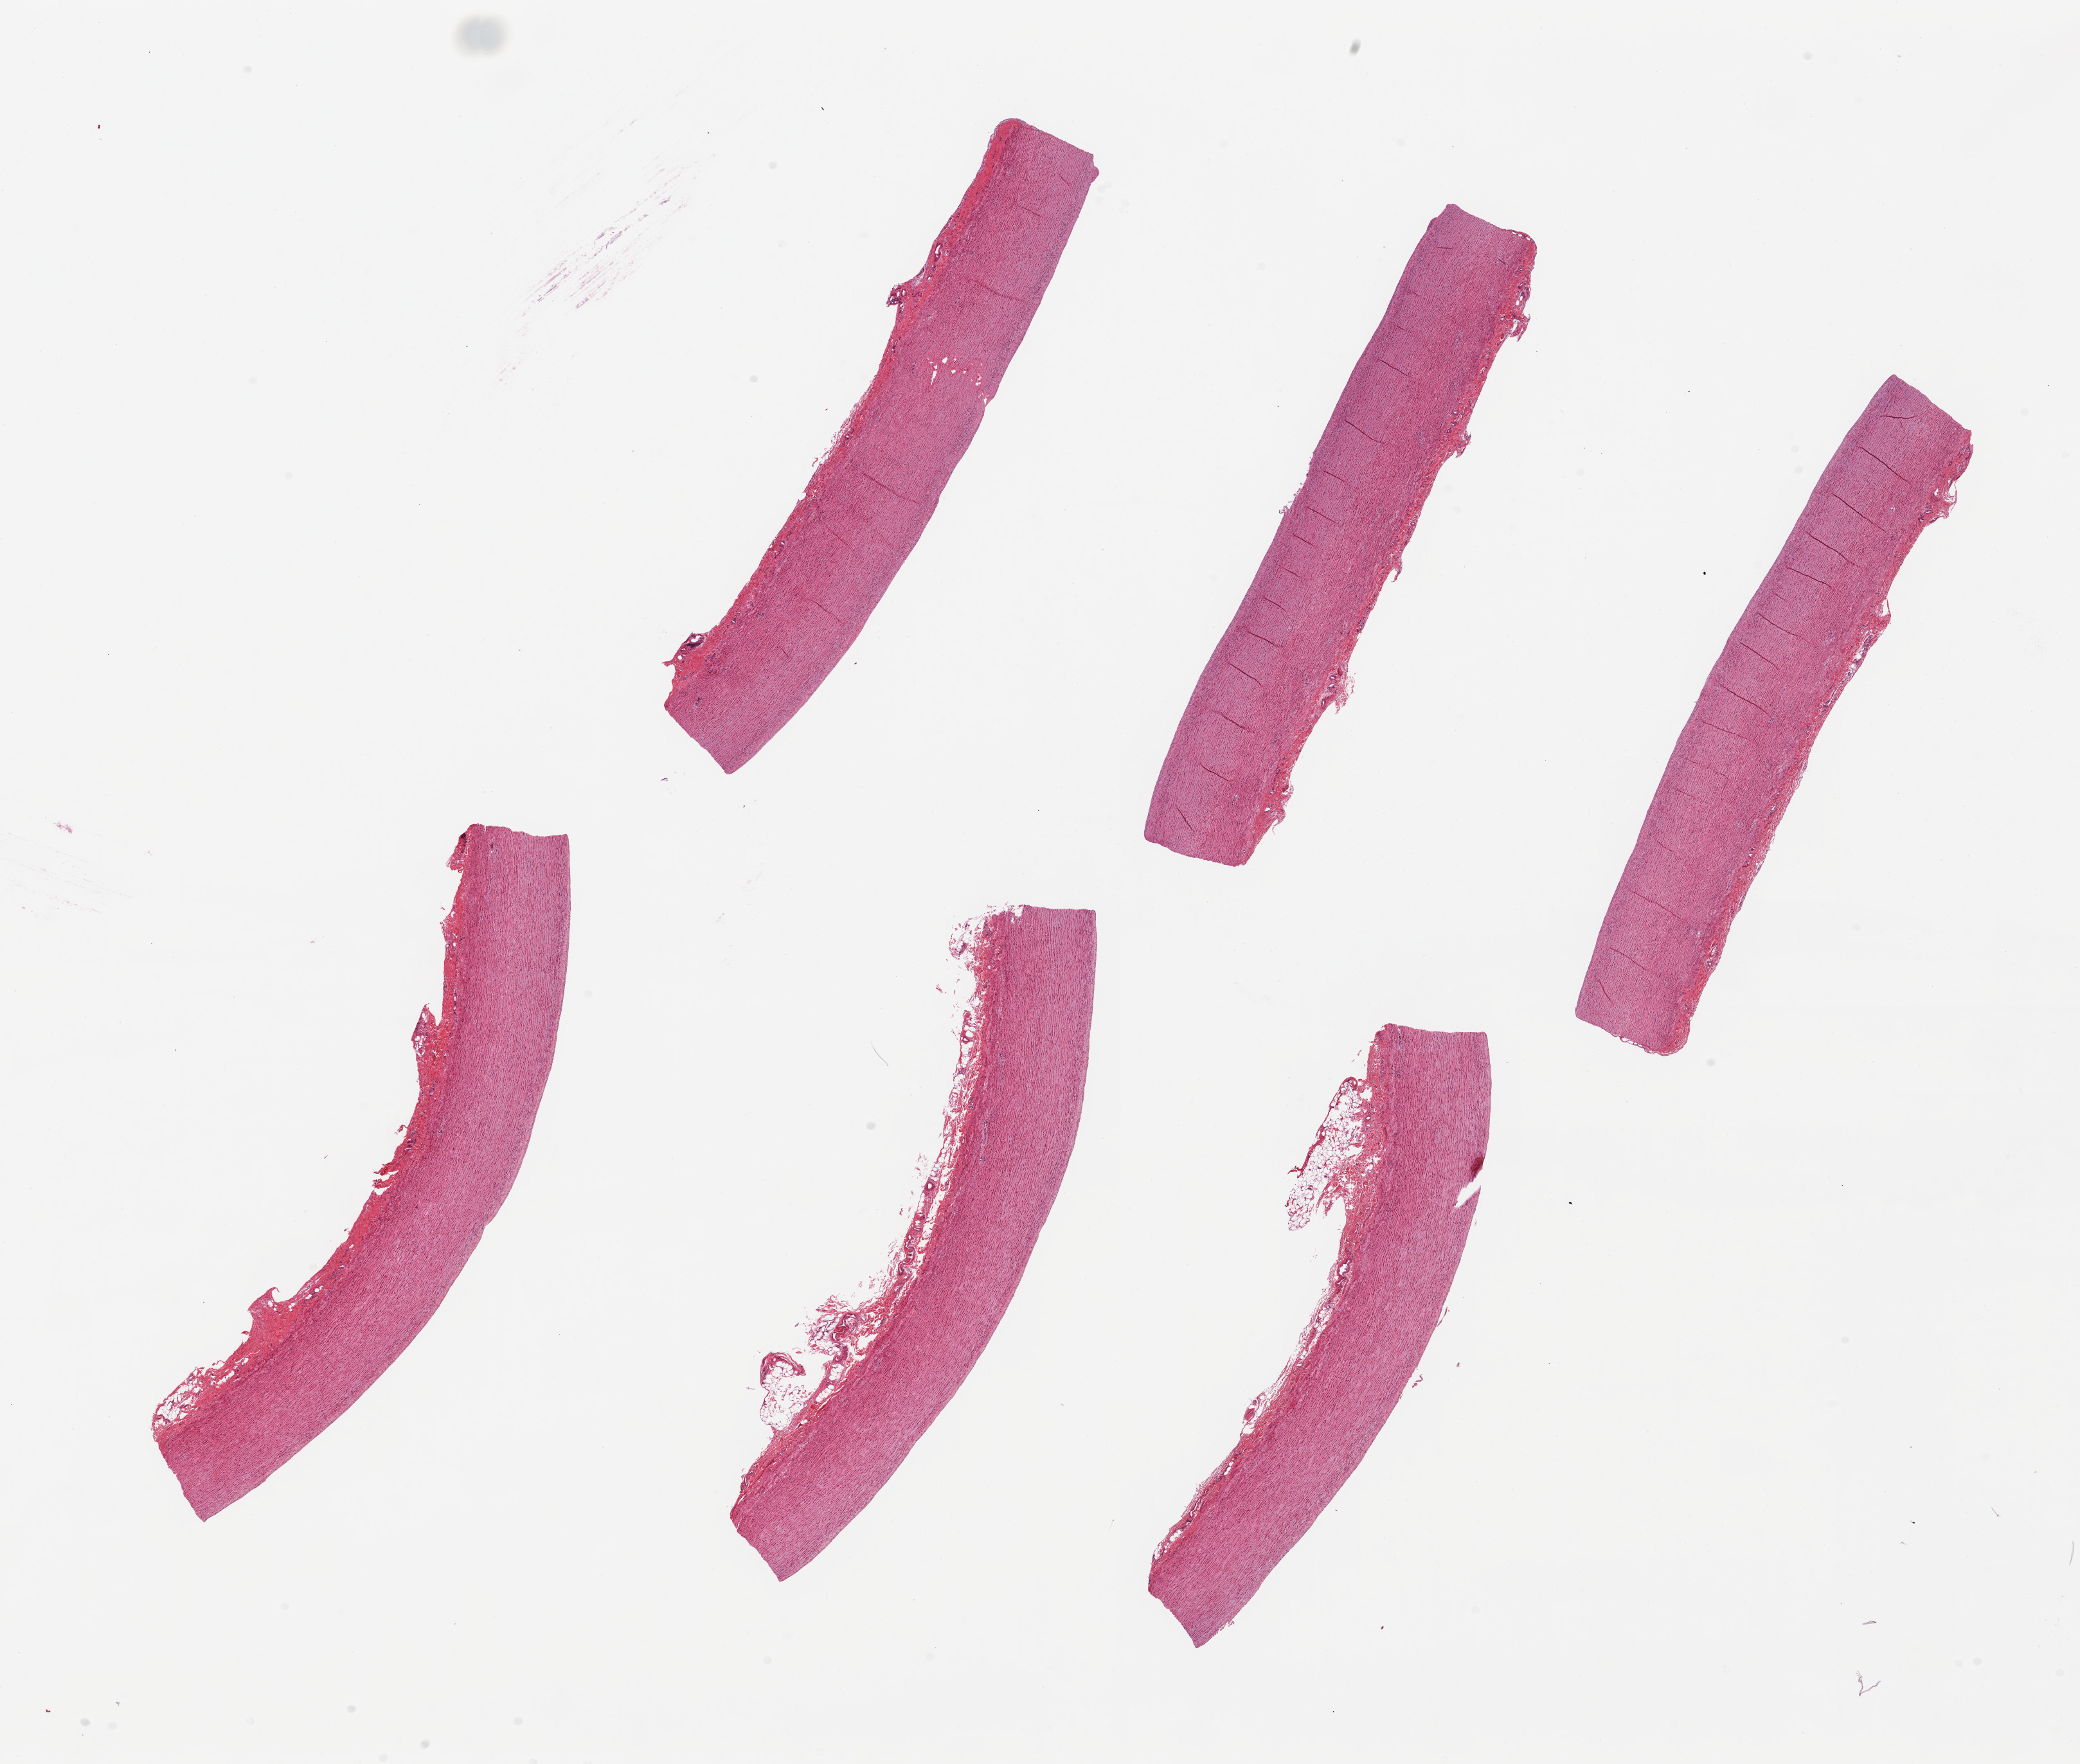
Digitized haematoxylin and eosin-stained section, brightfield — low-resolution overview of the scanned area, about 25.6 x 21.7 mm; PAXgene-fixed, paraffin-embedded tissue; sampled site (target tissue): aorta; tissue donor sample. Male donor.
- review note (as recorded): 6 pieces ~9x1.5mm. Minimal atherosis